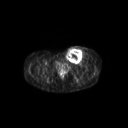
FDG PET of an extremity soft-tissue mass (from a PET/CT study), one axial slice; slice 61 of 267 in the series (ordered by position); 3.27 mm slice thickness; 128 × 128 image matrix, field of view 600 × 600 mm. Female patient, age 24 years. From the clinical record (not read from this slice): histological type: leiomyosarcoma; grade: high; site of the primary tumour: groin.
Annotated regions visible in this slice (expert contour drawn on MRI and transferred to this co-registered scan by the dataset authors):
- gross tumour volume including surrounding oedema: bounding box [x1, y1, x2, y2] px = [64, 46, 89, 64]
- gross tumour volume (mass): [64, 47, 83, 63]